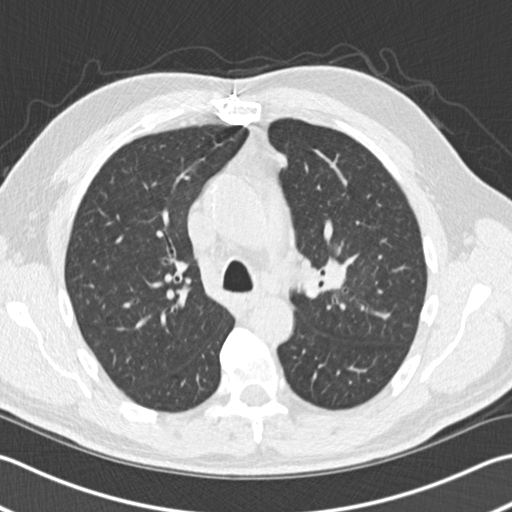
Axial slice from a low-dose chest CT screening exam. Third annual screen. Lung window (W 1500 / L -600 HU). 2 mm slice thickness. Slice 51 of 153 in the series. Male, age 65 years at enrolment. Former smoker at enrolment.
• Lesion marked by an expert reader, bounding box <307,239,371,303> (left, top, right, bottom; pixels).
• The screening reader recorded 4 non-calcified nodules or masses ≥4 mm on this exam (left upper lobe, left upper lobe, left lower lobe, right middle lobe); which of them this box marks is not recorded.
• Official screen result: positive, other.
• Lung cancer was diagnosed 196 days after this screen: acinar cell carcinoma, left upper lobe, stage IA (AJCC 6th edition), 25 mm at pathology.